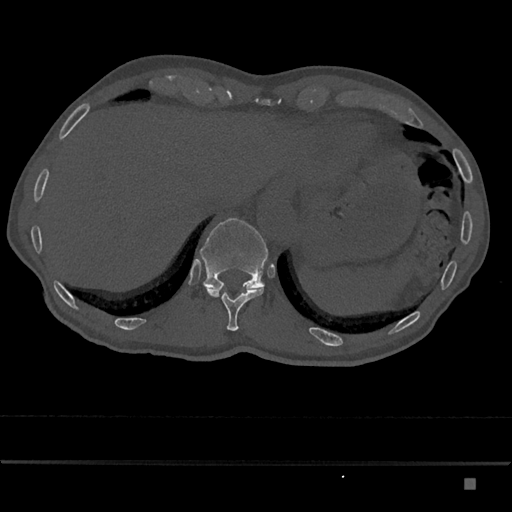
CT including the spine, one axial slice. Position 648 of 797 along the scan axis. Bone window (W 1800 / L 400 HU). 0.5 mm slice thickness. 512 × 512 image matrix, field of view 390 × 390 mm. Patient: male, 72 years. From the clinical record (not read from this slice): primary cancer: prostate.
Structures marked on this image (semi-automatically segmented with operator editing):
- T11 vertebra: bounding box [x1, y1, x2, y2] px = [207, 287, 264, 331]
- T12 vertebra: [199, 218, 268, 289]